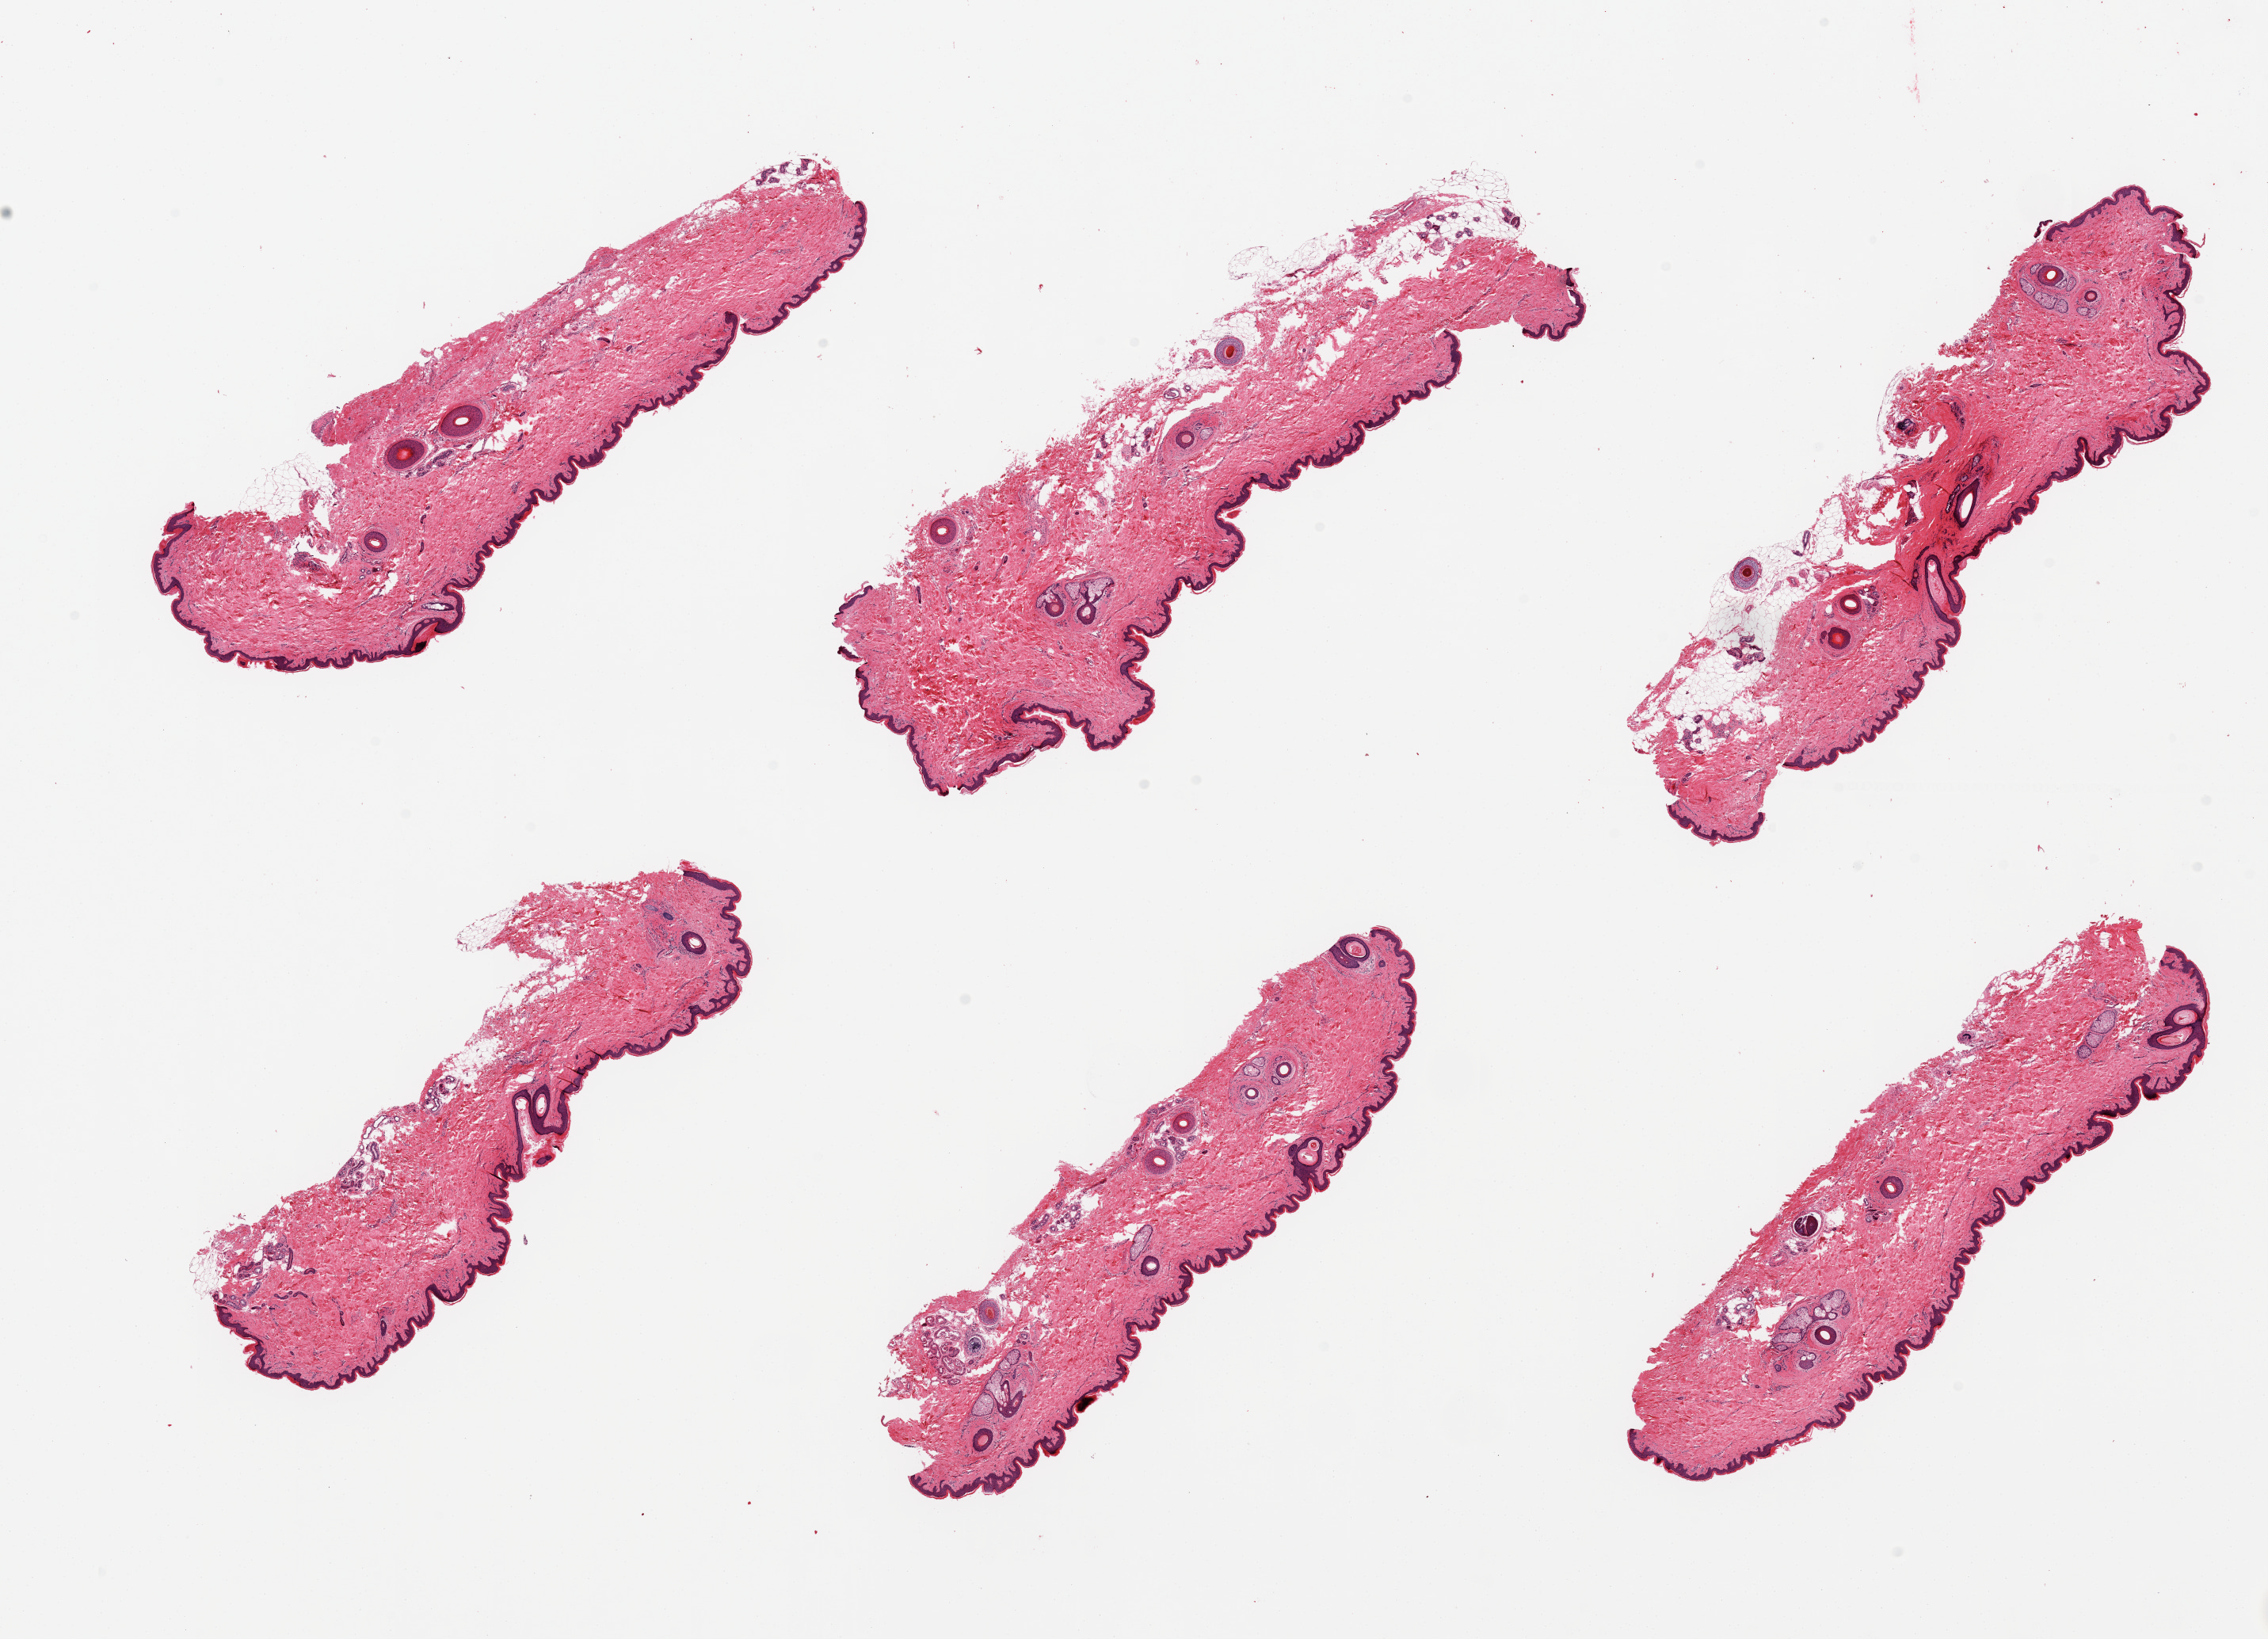
Digitized hematoxylin and eosin (H&E)-stained section, brightfield — shown as a low-resolution overview of the whole scanned area (about 22.6 x 16.4 mm, from a 20x scan). PAXgene-fixed, paraffin-embedded tissue. Target tissue: skin of suprapubic region. Donor tissue sample.
Pathologist's review note for this sample: 6 pieces; well trimmed, but contains up to 10 hair follicles per piece; 5-10% dermal fat.